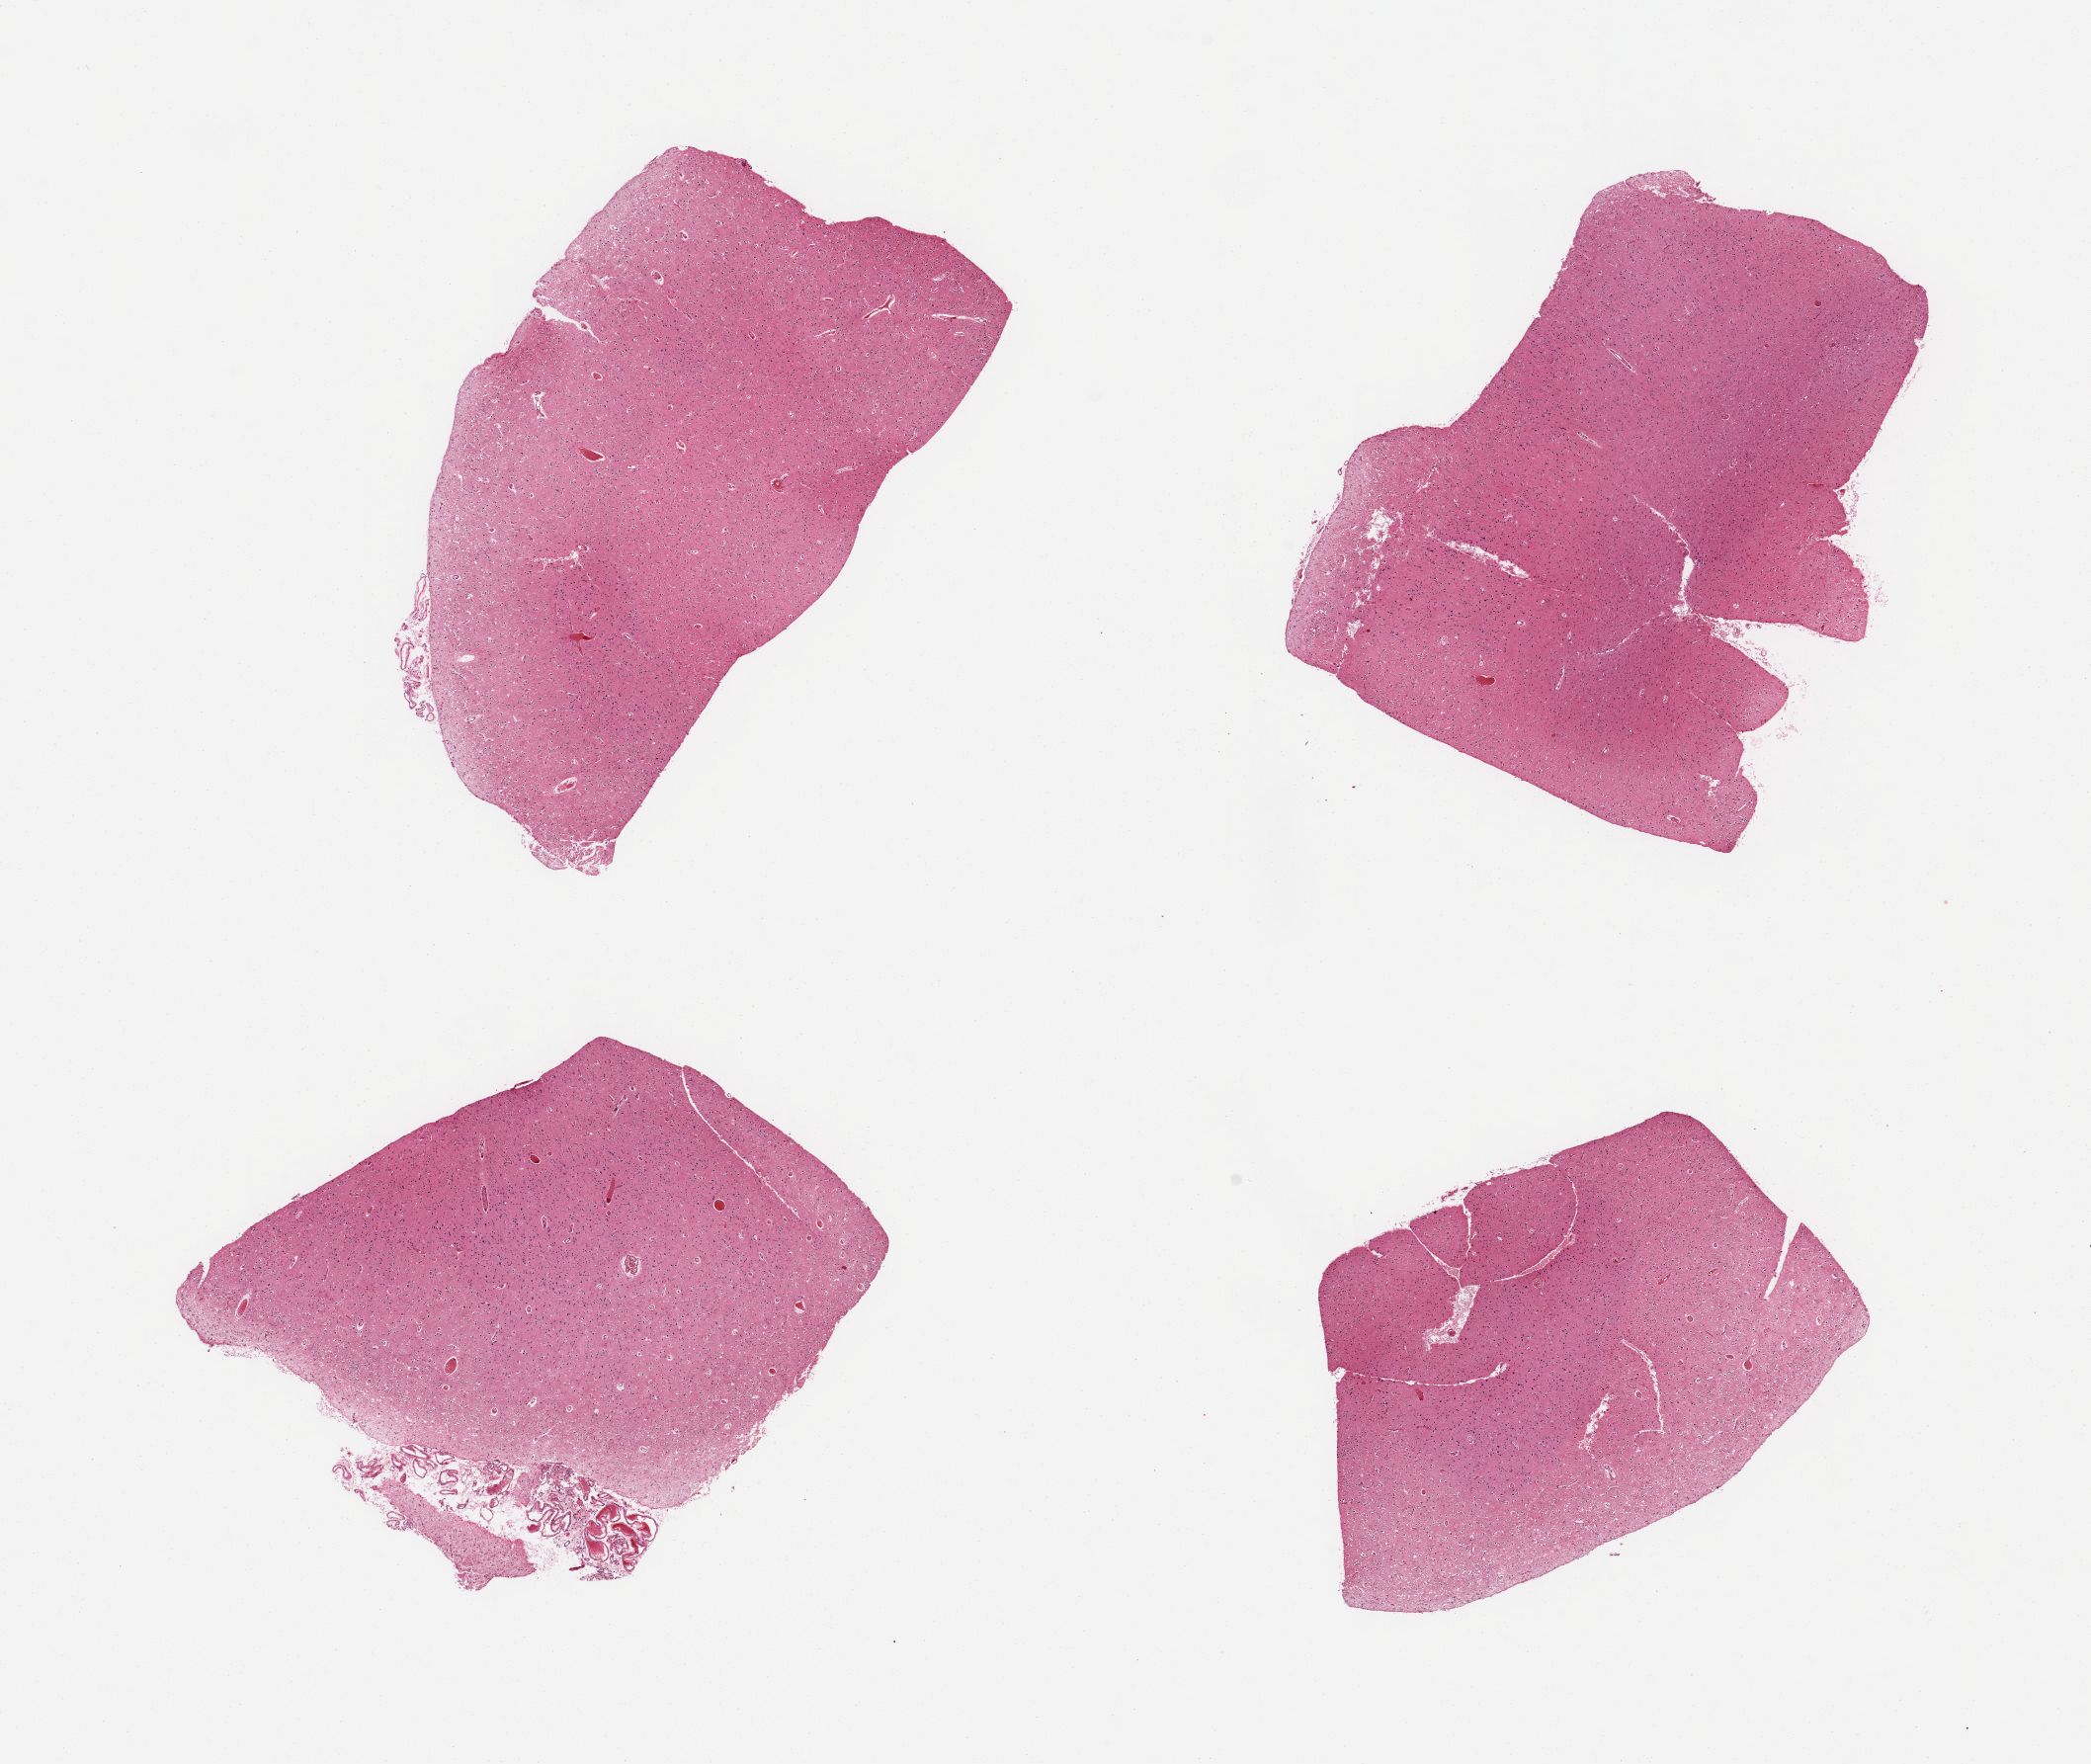
H&E whole-slide image, shown as a low-resolution overview of the whole scanned area (about 16.7 x 14.1 mm, from a 20x scan), PAXgene-fixed, paraffin-embedded tissue, target tissue: cerebral cortex, tissue donor sample. Female donor.
Reviewer comment on this tissue sample: 4 pieces; focus of adherent meninges.